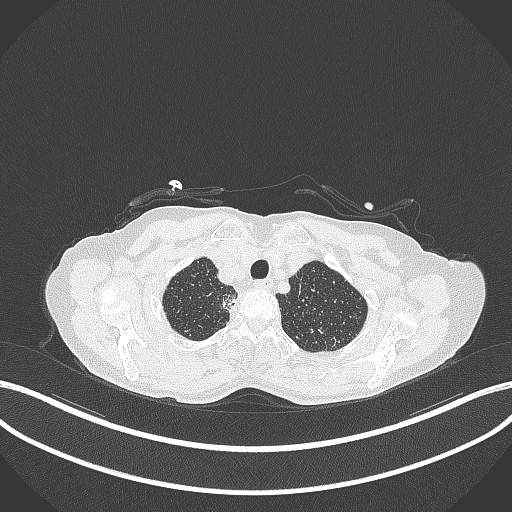
Chest CT, one axial slice. Reconstruction kernel B70f. 120 kVp. Lung window (W 1500 / L -600 HU). 1 mm slice thickness. 512 × 512 image matrix. Patient: female, 75 years. From the clinical record (not read from this slice): clinical TNM (as recorded): T1c N1 M1.
Outlined on this slice (rectangle marked by the reading radiologist):
- lung tumour (recorded histology: adenocarcinoma): bounding box <219,287,243,317> (left, top, right, bottom; pixels)